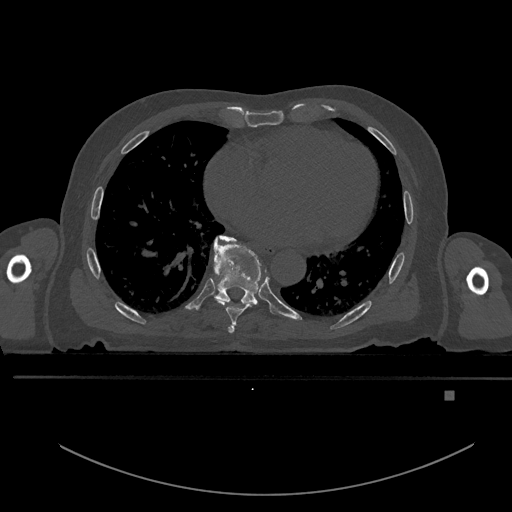
CT including the spine, one axial slice; position 227 of 969 along the scan axis; bone window (W 1800 / L 400 HU); 0.5 mm slice thickness; 512 × 512 image matrix, field of view 456 × 456 mm. Male patient, age 82 years. From the clinical record (not read from this slice): primary cancer: prostate; vertebrae with lytic lesions (as recorded): T11, T9, T8, T2.
Structures marked on this image (semi-automatically segmented with operator editing):
- T6 vertebra: box from (x=228, y=326) to (x=234, y=333) px
- T7 vertebra: (x=218, y=235)–(x=267, y=325)
- T8 vertebra: (x=213, y=237)–(x=262, y=308)